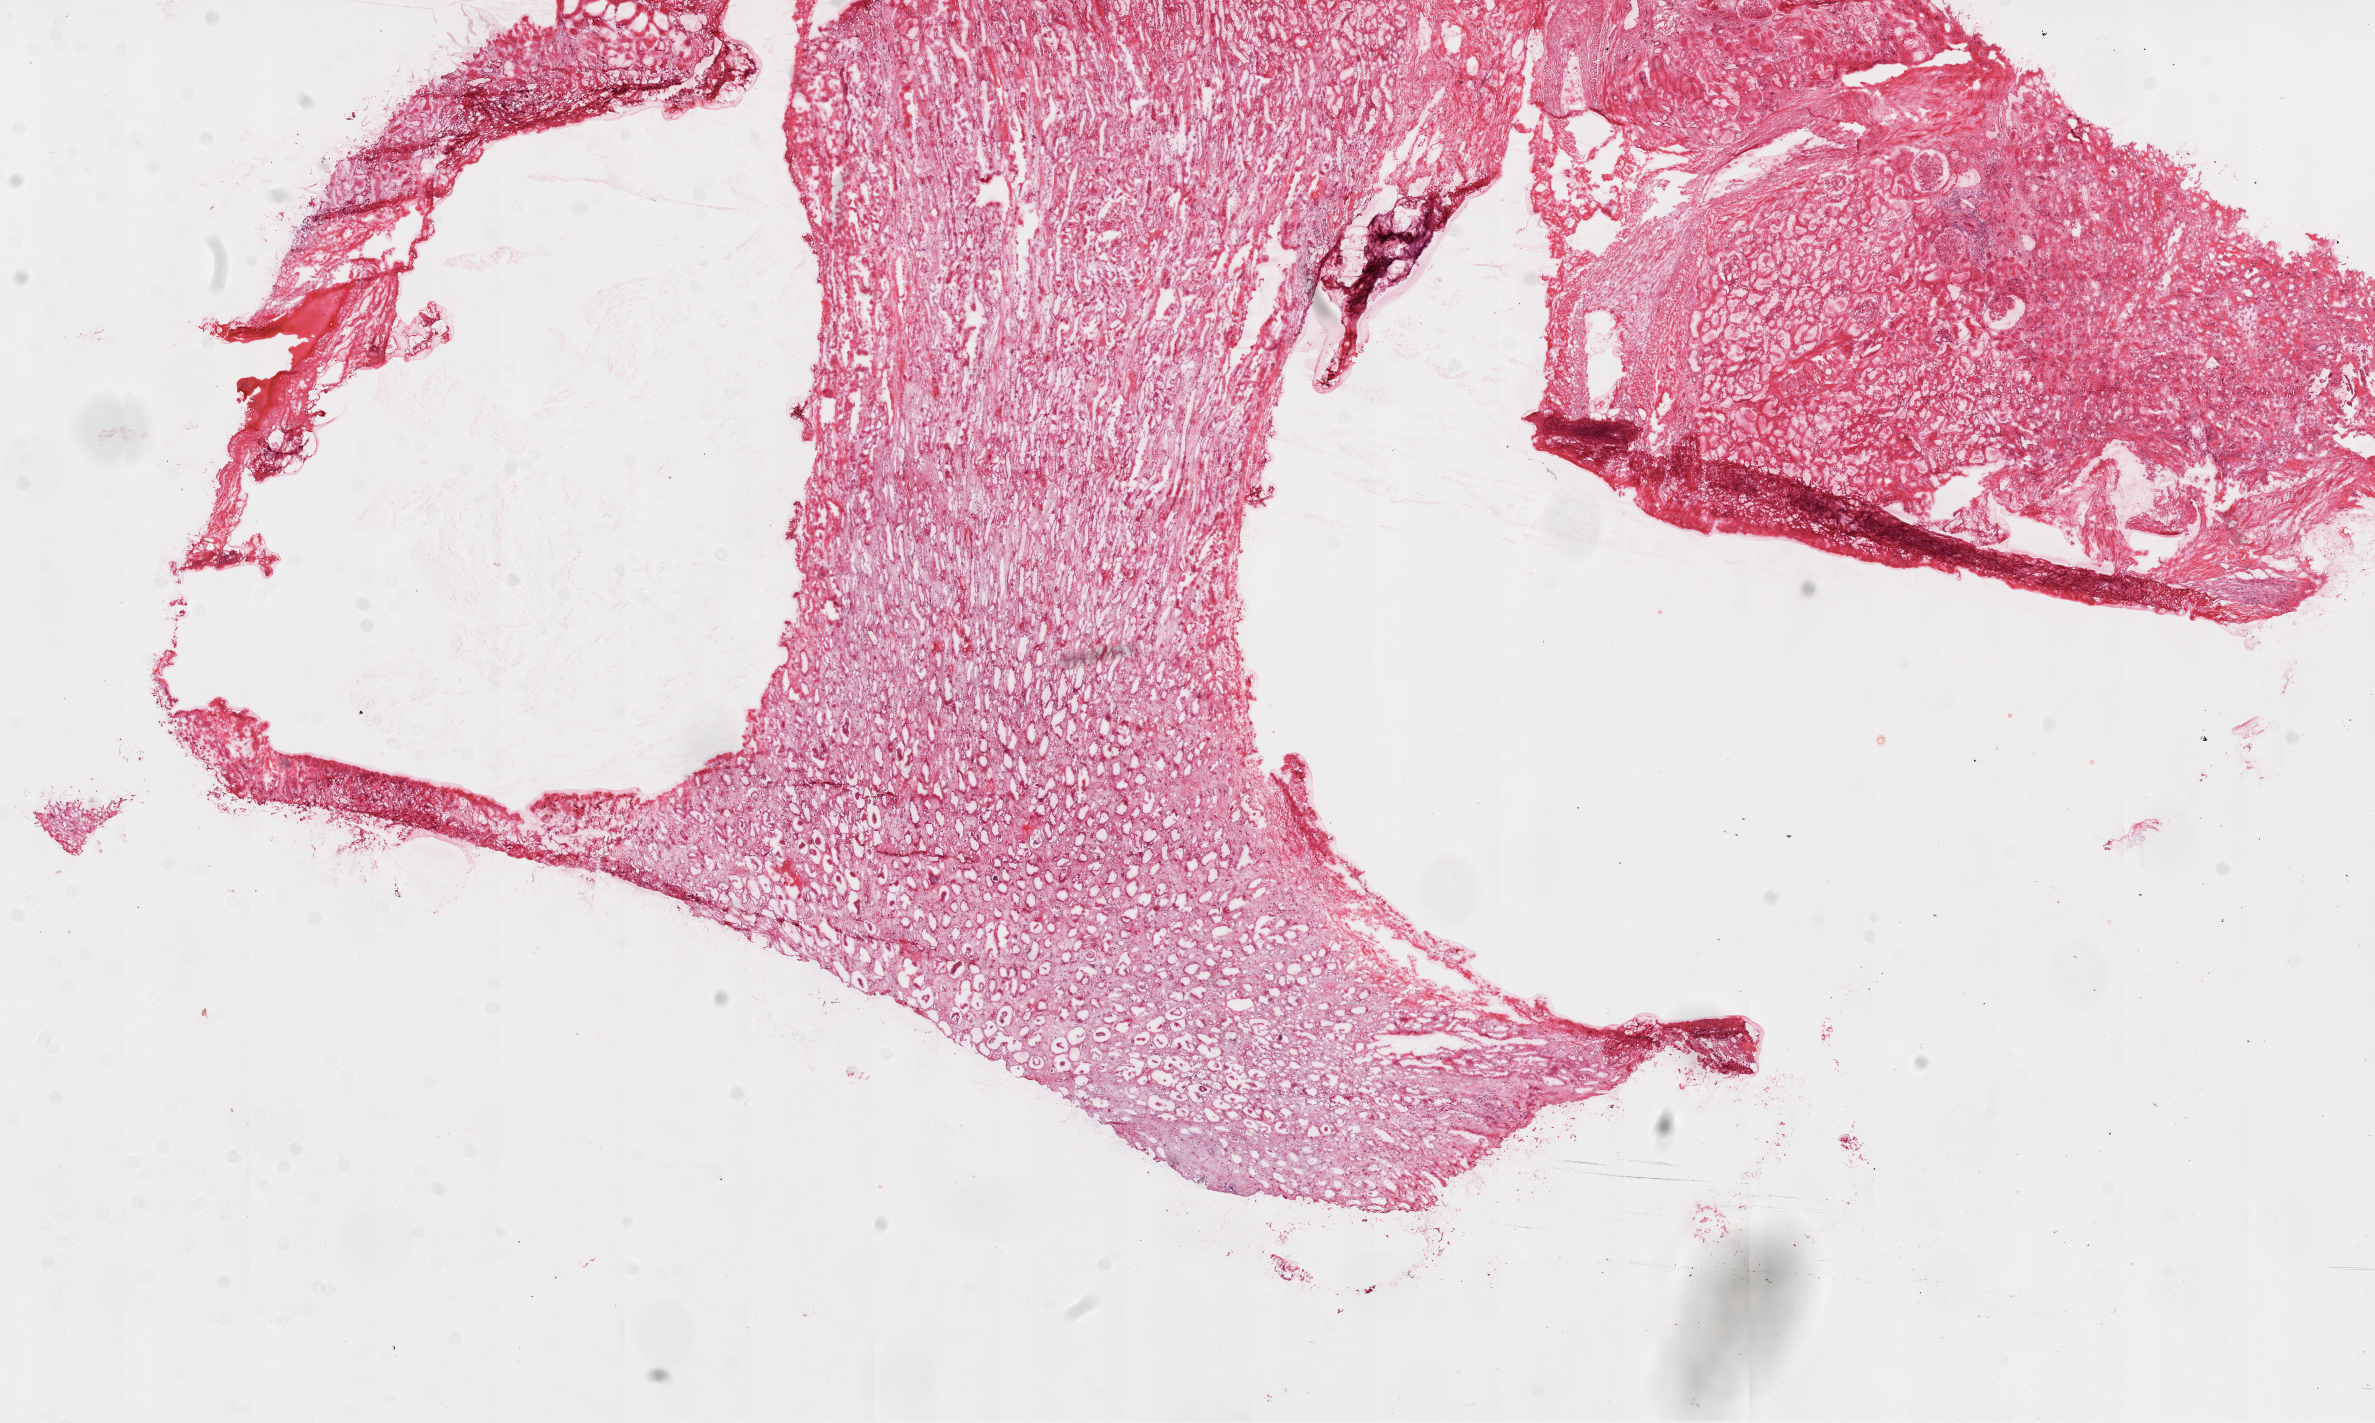
Whole-slide histology image, H&E-stained, whole scanned area (about 19.1 x 11.4 mm) shown as a low-resolution overview. Frozen section. Kidney, solid tissue normal (non-tumour tissue) sample. Male patient; age at initial diagnosis 79 years.
This section: solid tissue normal (non-tumour) sample from the same patient. Patient diagnosis: Clear cell adenocarcinoma, NOS.